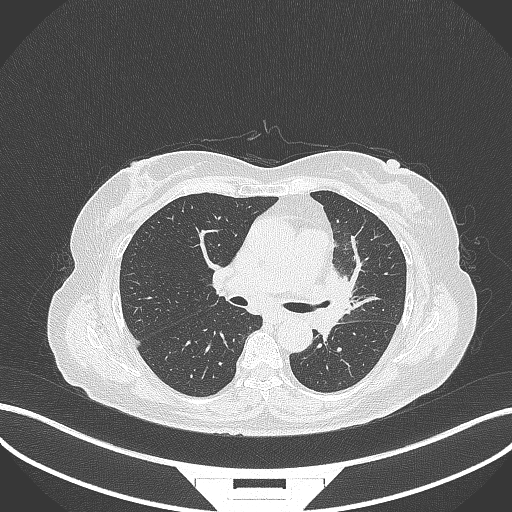
Chest CT, one axial slice; position 194 of 382 along the scan axis; reconstruction kernel B70f; lung window (W 1500 / L -600 HU); 512 × 512 image matrix, field of view 400 × 400 mm. Female patient, age 64 years. Case-level facts recorded for this patient, not image findings: clinical TNM (as recorded): T2a N2 M0.
Outlined on this slice (bounding box drawn by a radiologist):
- lung tumour (recorded histology: adenocarcinoma): bounding box (x1, y1, x2, y2) in pixels: (317, 256, 363, 336)